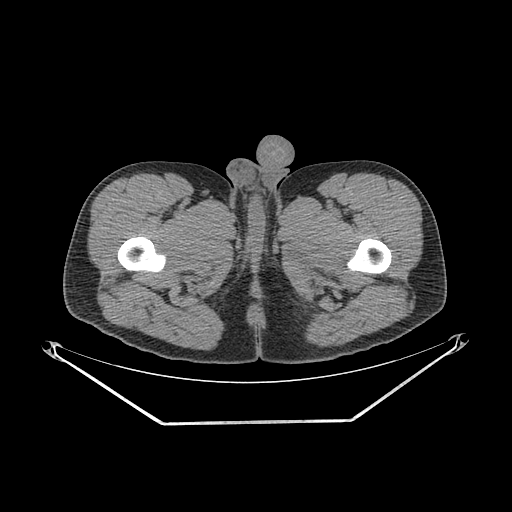
CT of an extremity soft-tissue mass (from a PET/CT study), one axial slice. Slice 267 of 267 in the series (ordered by position). Soft-tissue window (W 400 / L 40 HU). 3.75 mm slice thickness. 512 × 512 image matrix, field of view 500 × 500 mm. Male patient. Case-level facts recorded for this patient, not image findings: histological type: extraskeletal osteosarcoma; grade: high; site of the primary tumour: left adductur.
Outlined on this slice (expert contour drawn on MRI and transferred to this co-registered scan by the dataset authors):
- gross tumour volume (mass): bounding box [x1, y1, x2, y2] px = [306, 199, 385, 295]